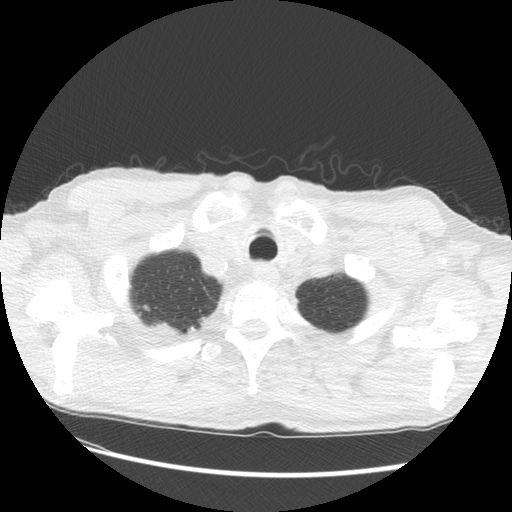
Low-dose screening chest CT, one axial slice. Slice 125 of 133 in the series (ordered by position). Lung window (W 1500 / L -600 HU). 512 × 512 image matrix, field of view 360 × 360 mm.
Outlined on this slice (expert manual segmentation):
- lesion 2 (tumor, upper lobe of right lung): bounding box <150,321,179,334> (left, top, right, bottom; pixels)